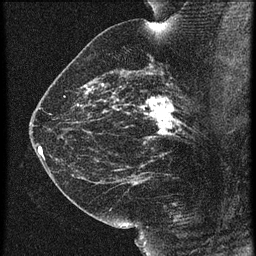
Breast MRI (dynamic contrast-enhanced), one sagittal slice; slice 36 of 60 in the series (ordered by position); 3 images stored at this slice position (order not interpretable as contrast timing); 1.5 T; TE 4.2 ms, TR 21.3 ms; 1.5 mm slice thickness; 256 × 256 image matrix, field of view 180 × 180 mm. Female patient, age 42 years. Case-level facts recorded for this patient, not image findings: setting: breast cancer imaged before/during neoadjuvant chemotherapy; receptor status: HER2-positive.
Outlined on this slice (semi-automatic segmentation, software-assisted and operator-edited):
- analysis volume of interest (the breast-tissue region the enhancement analysis was run in; not a lesion): bounding box (x1, y1, x2, y2) in pixels: (122, 82, 195, 147)
- tumour enhancement mask (voxels above the 90 % enhancement threshold inside the analysis volume of interest): (133, 96, 180, 137)